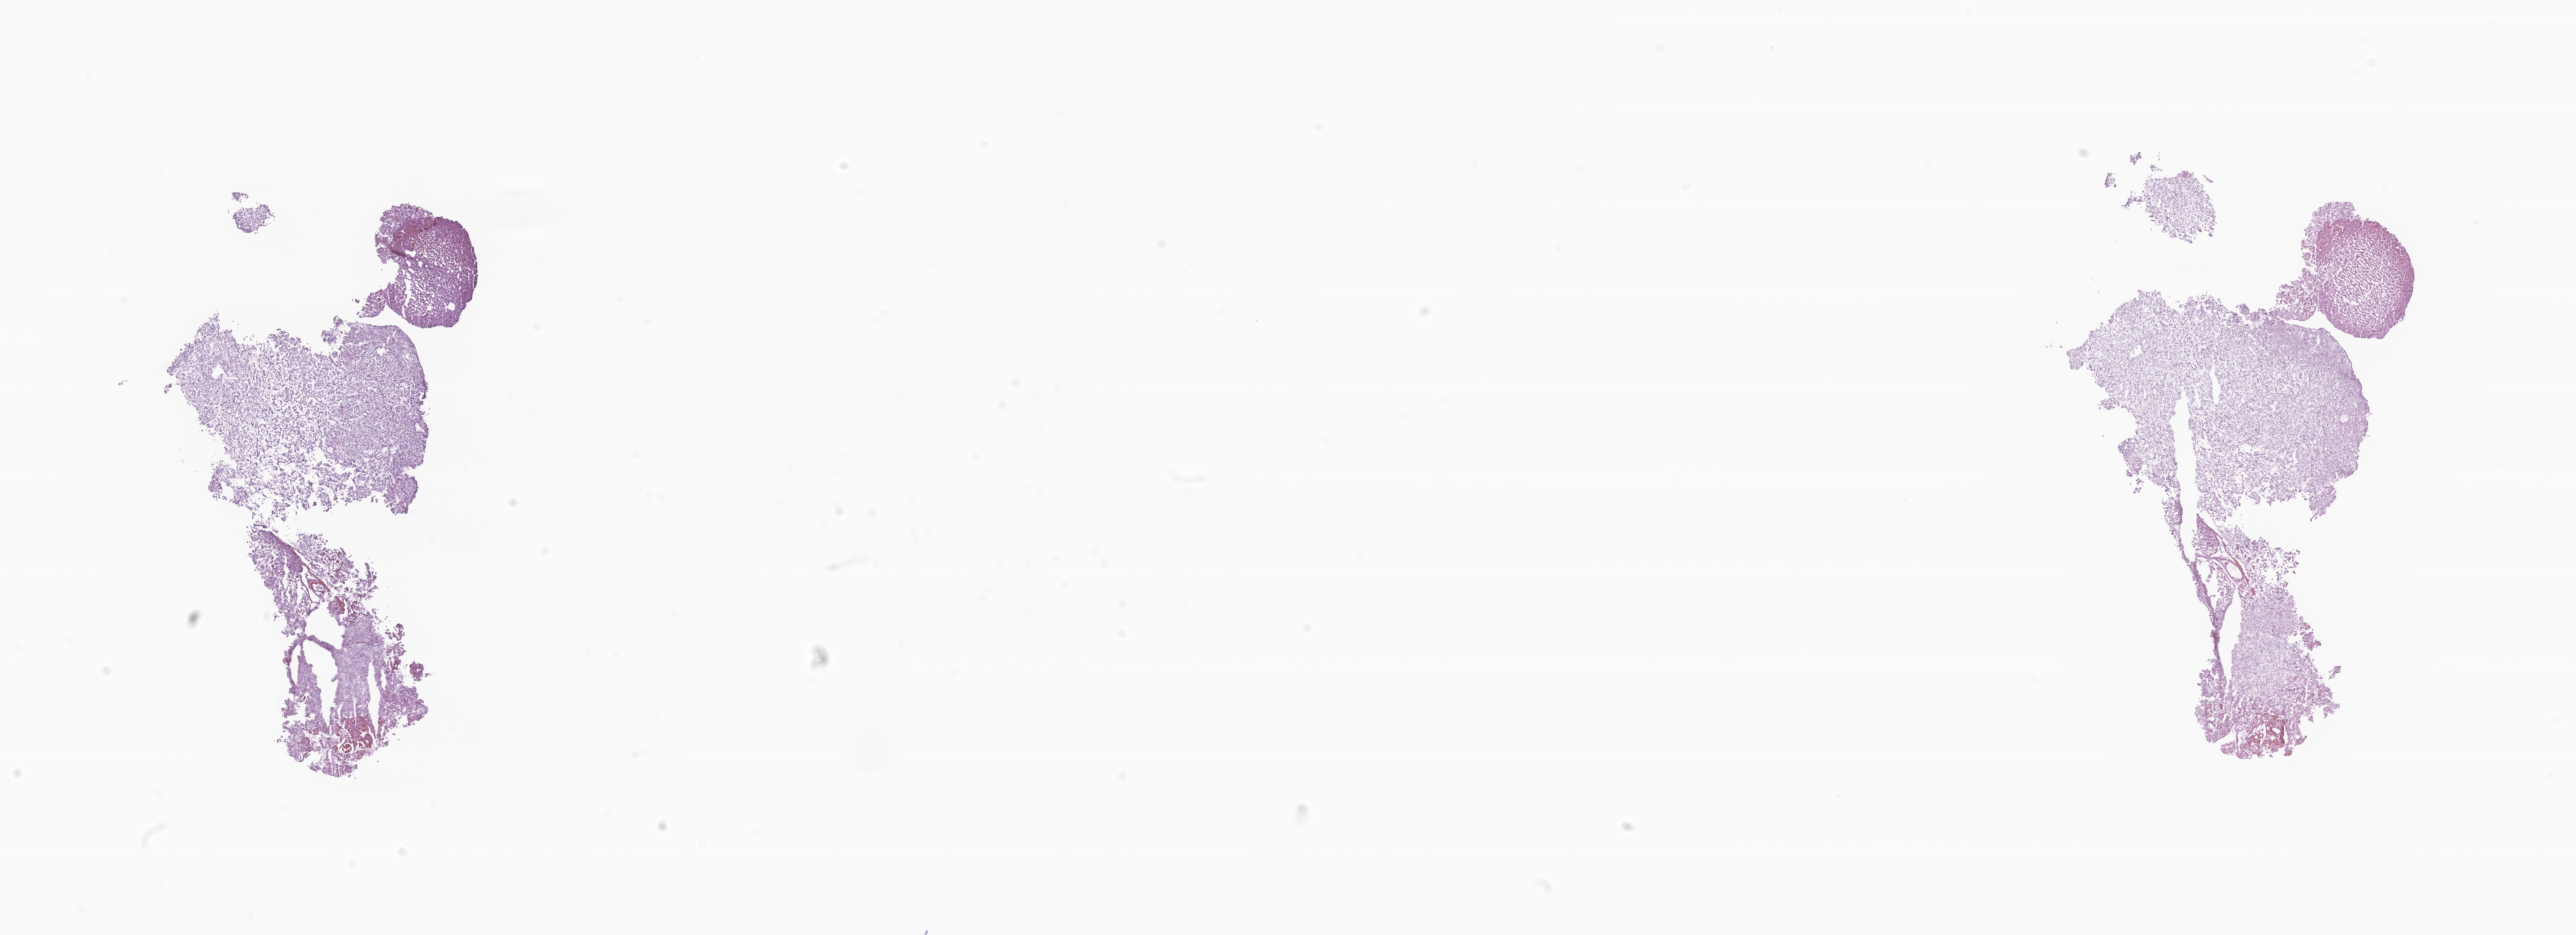
Whole-slide image, hematoxylin and eosin (H&E) stain of tumor tissue from the frontal lobe — shown as a low-resolution overview of the whole scanned area (about 29.8 x 10.8 mm), cryosection (OCT / tissue freezing medium). Patient female; age 126 months (10 years 6 months).
Diagnosis: Oligoastrocytoma, NOS.